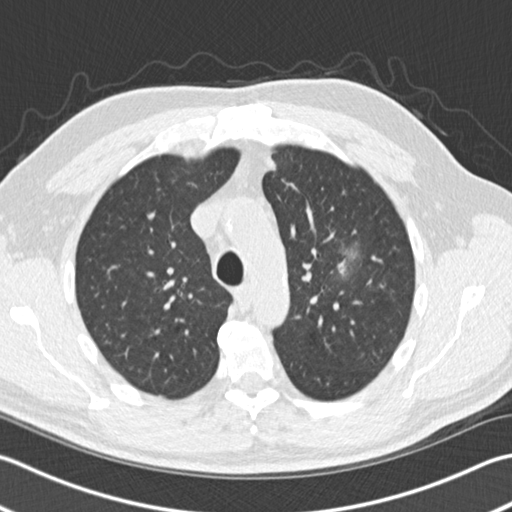
Low-dose screening chest CT, axial slice, third screening round (two years after baseline), lung window (W 1500 / L -600 HU), 2 mm slice thickness, 120 kVp, slice 40 of 153 in the series. Male participant, aged 65 years at enrolment. Former smoker at enrolment.
Lesion marked by an expert reader, bounding box (x1, y1, x2, y2) in pixels: (306, 241, 370, 306). The screening reader recorded 4 non-calcified nodules or masses ≥4 mm on this exam; which of them this box marks is not recorded. Official screen result: positive, other. Participant outcome: lung cancer diagnosed 196 days after this screen — acinar cell carcinoma, left upper lobe, stage IA (AJCC 6th edition), 25 mm at pathology.